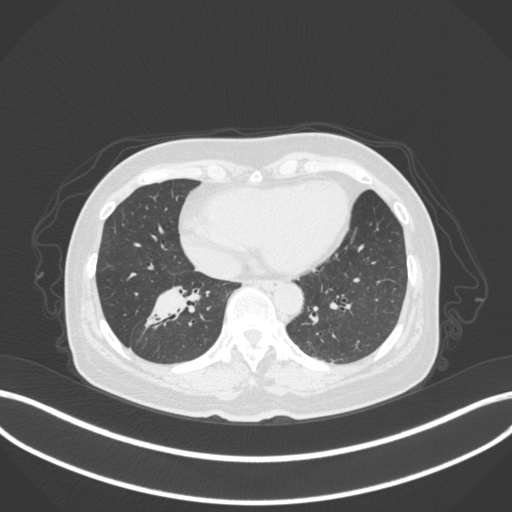
Chest CT, one axial slice. Slice 133 of 429 in the series (ordered by position). Reconstruction kernel B31f. Lung window (W 1500 / L -600 HU). 1 mm slice thickness. 512 × 512 image matrix, field of view 400 × 400 mm. Female patient, age 67 years. From the clinical record (not read from this slice): clinical TNM (as recorded): T1c N1 M0; histopathological grade: G2-3.
Structures marked on this image (rectangle marked by the reading radiologist):
- lung tumour (recorded histology: adenocarcinoma): bounding box (x1, y1, x2, y2) in pixels: (144, 279, 205, 334)